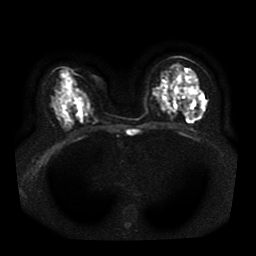
Breast MRI, one axial slice. Slice 19 of 41 in the series (ordered by position). Diffusion-weighted series; image 2 of 4 stored at this slice position (different b-values; order by instance number). 1.5 T. 5 mm slice thickness. 256 × 256 image matrix, field of view 330 × 330 mm. Female patient.
Outlined on this slice (outlined manually by an expert reader):
- tumour on diffusion-weighted imaging: bounding box [x1, y1, x2, y2] px = [179, 87, 202, 115]